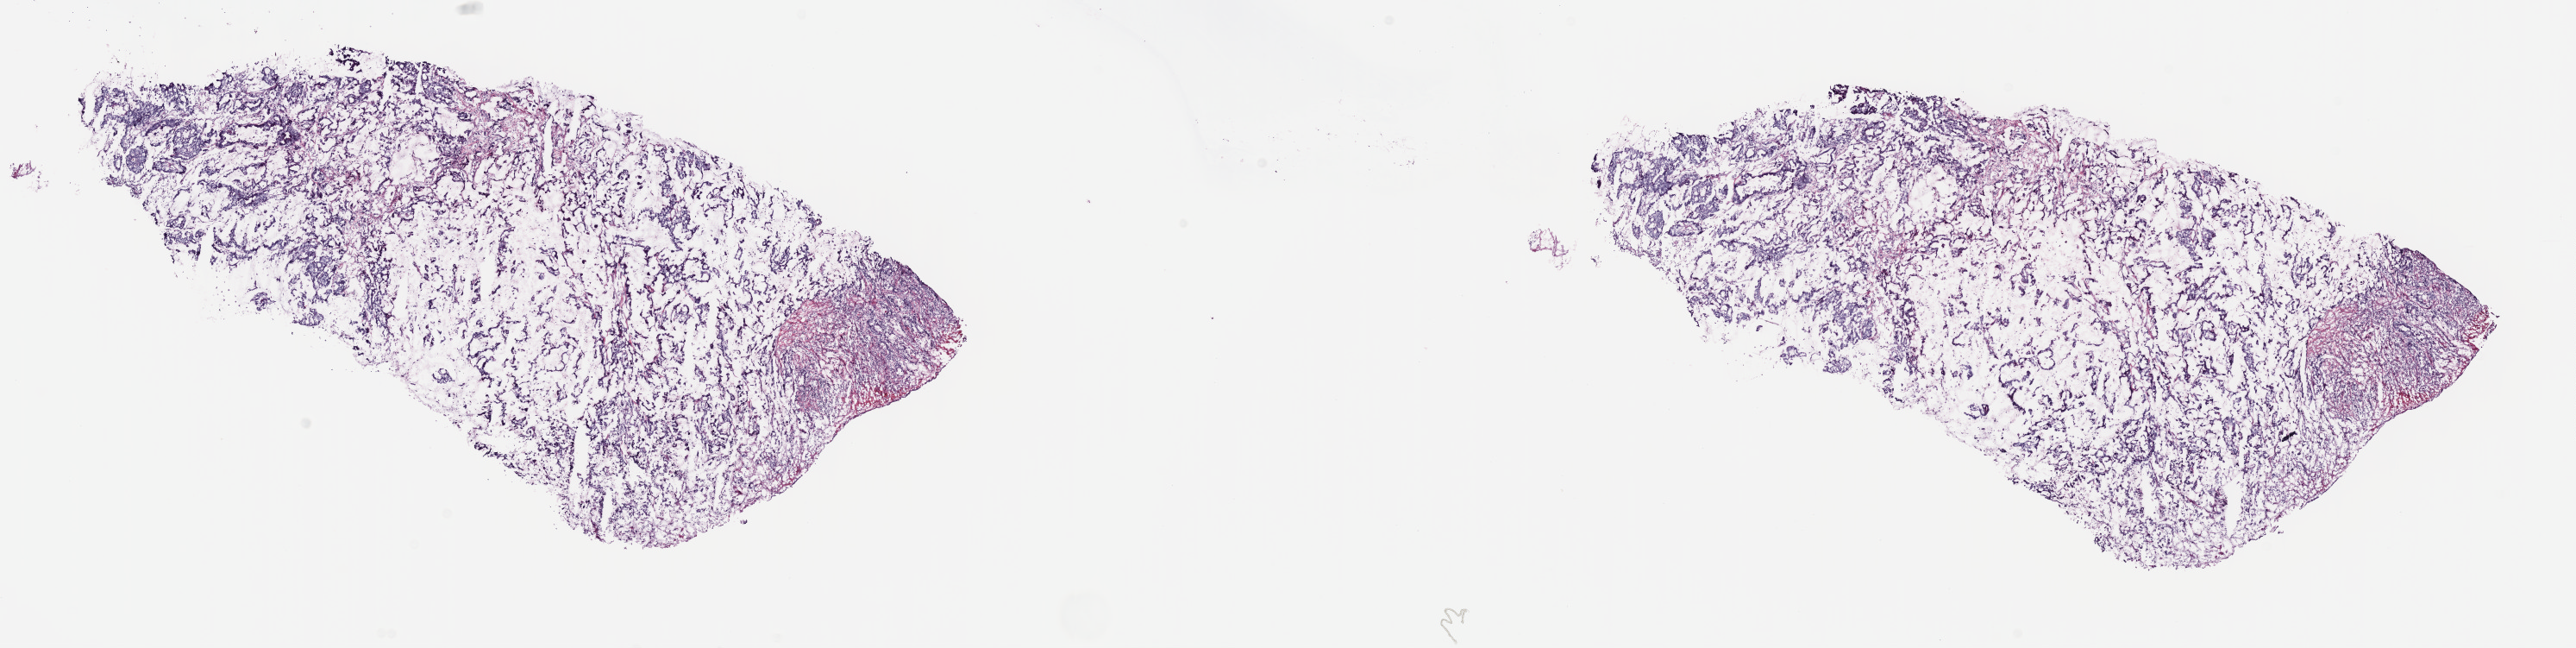
H&E-stained whole-slide image, a low-resolution overview of the entire scanned area, about 24.2 x 6.1 mm (from a 40x scan); frozen section from the top of the tissue portion; esophagus, primary tumour sample. Female, age 72 years at initial diagnosis. Histologic grade: G3 (poorly differentiated). Pathologist review of this section (percent, as recorded): tumour cells 70%, tumour nuclei 70%, normal cells 0%, stromal cells 30%, necrosis 0%. Inflammatory infiltration, as recorded: lymphocyte infiltration 80%, monocyte infiltration 20%, neutrophil infiltration 0%.
AJCC pathologic stage: IIB (6th edition). Pathologic diagnosis: Adenocarcinoma, NOS (lower third of esophagus). Lymph nodes positive (case pathology): 2 of 22 examined.